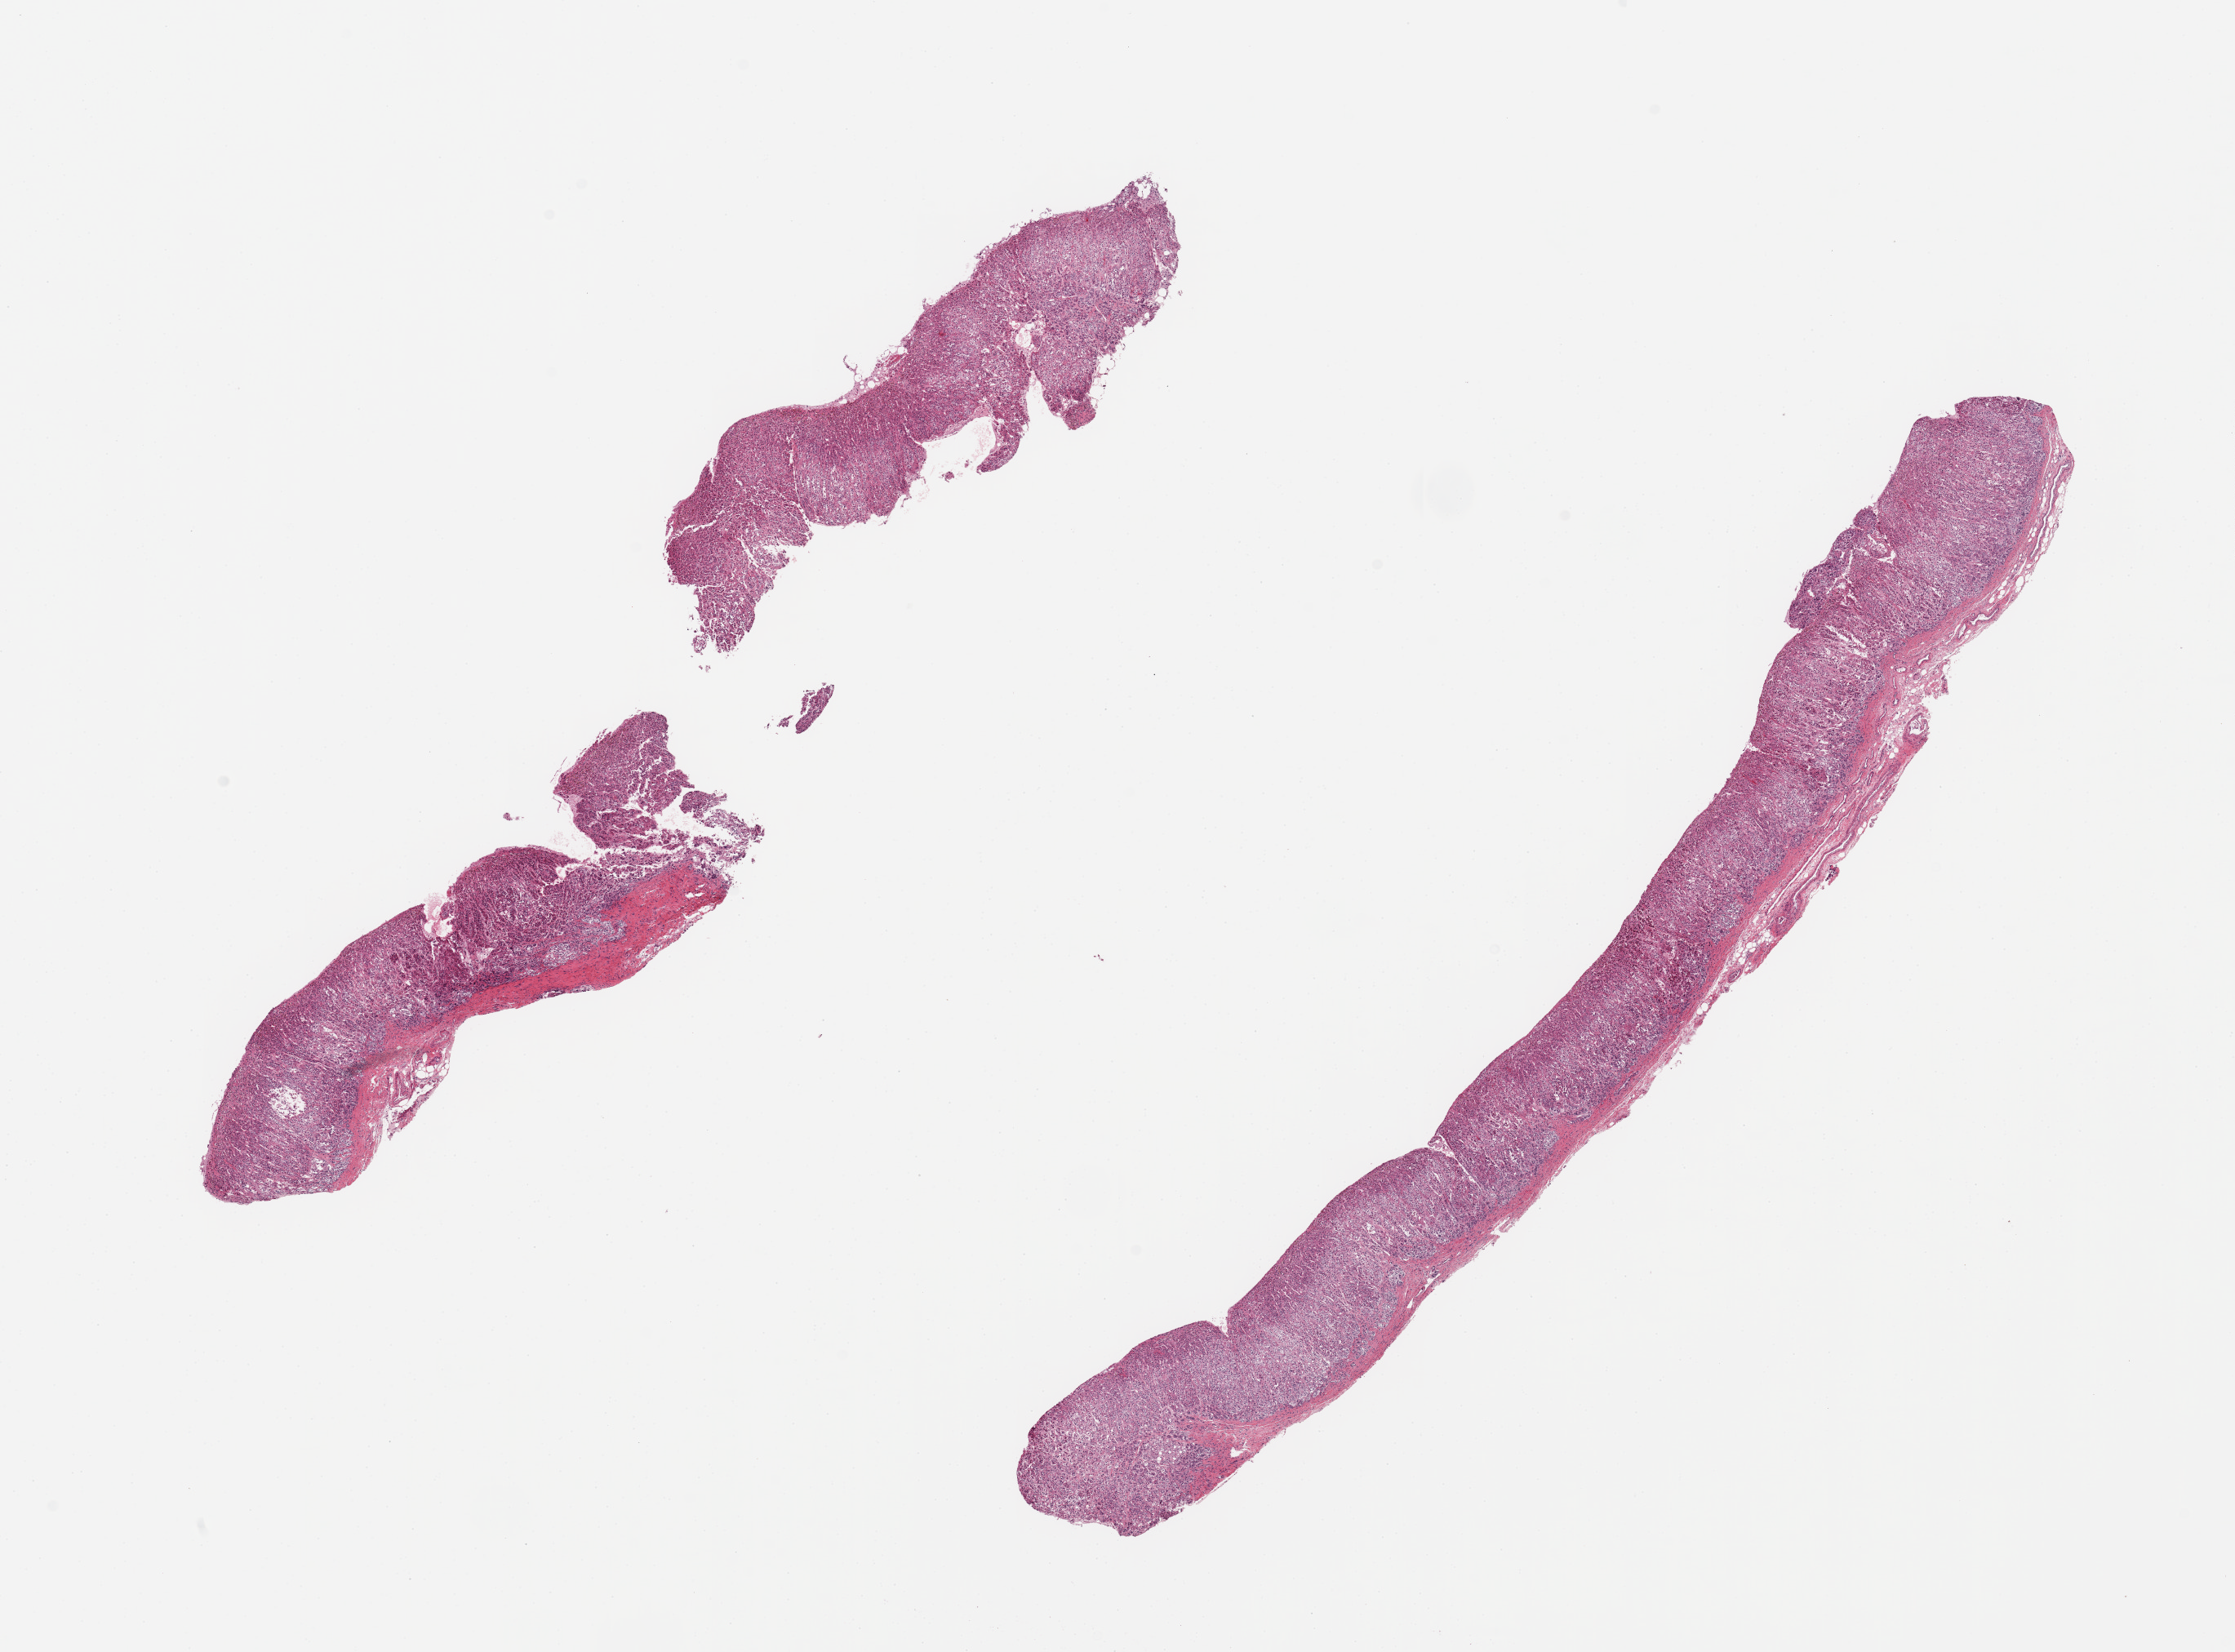
Whole-slide image, haematoxylin and eosin stain, a low-resolution overview of the entire scanned area, about 21.7 x 16.0 mm. PAXgene-fixed, paraffin-embedded tissue. Sampled site (target tissue): adrenal gland. Tissue donor sample. Donor: female.
- review note (as recorded): 2 pieces; atrophic